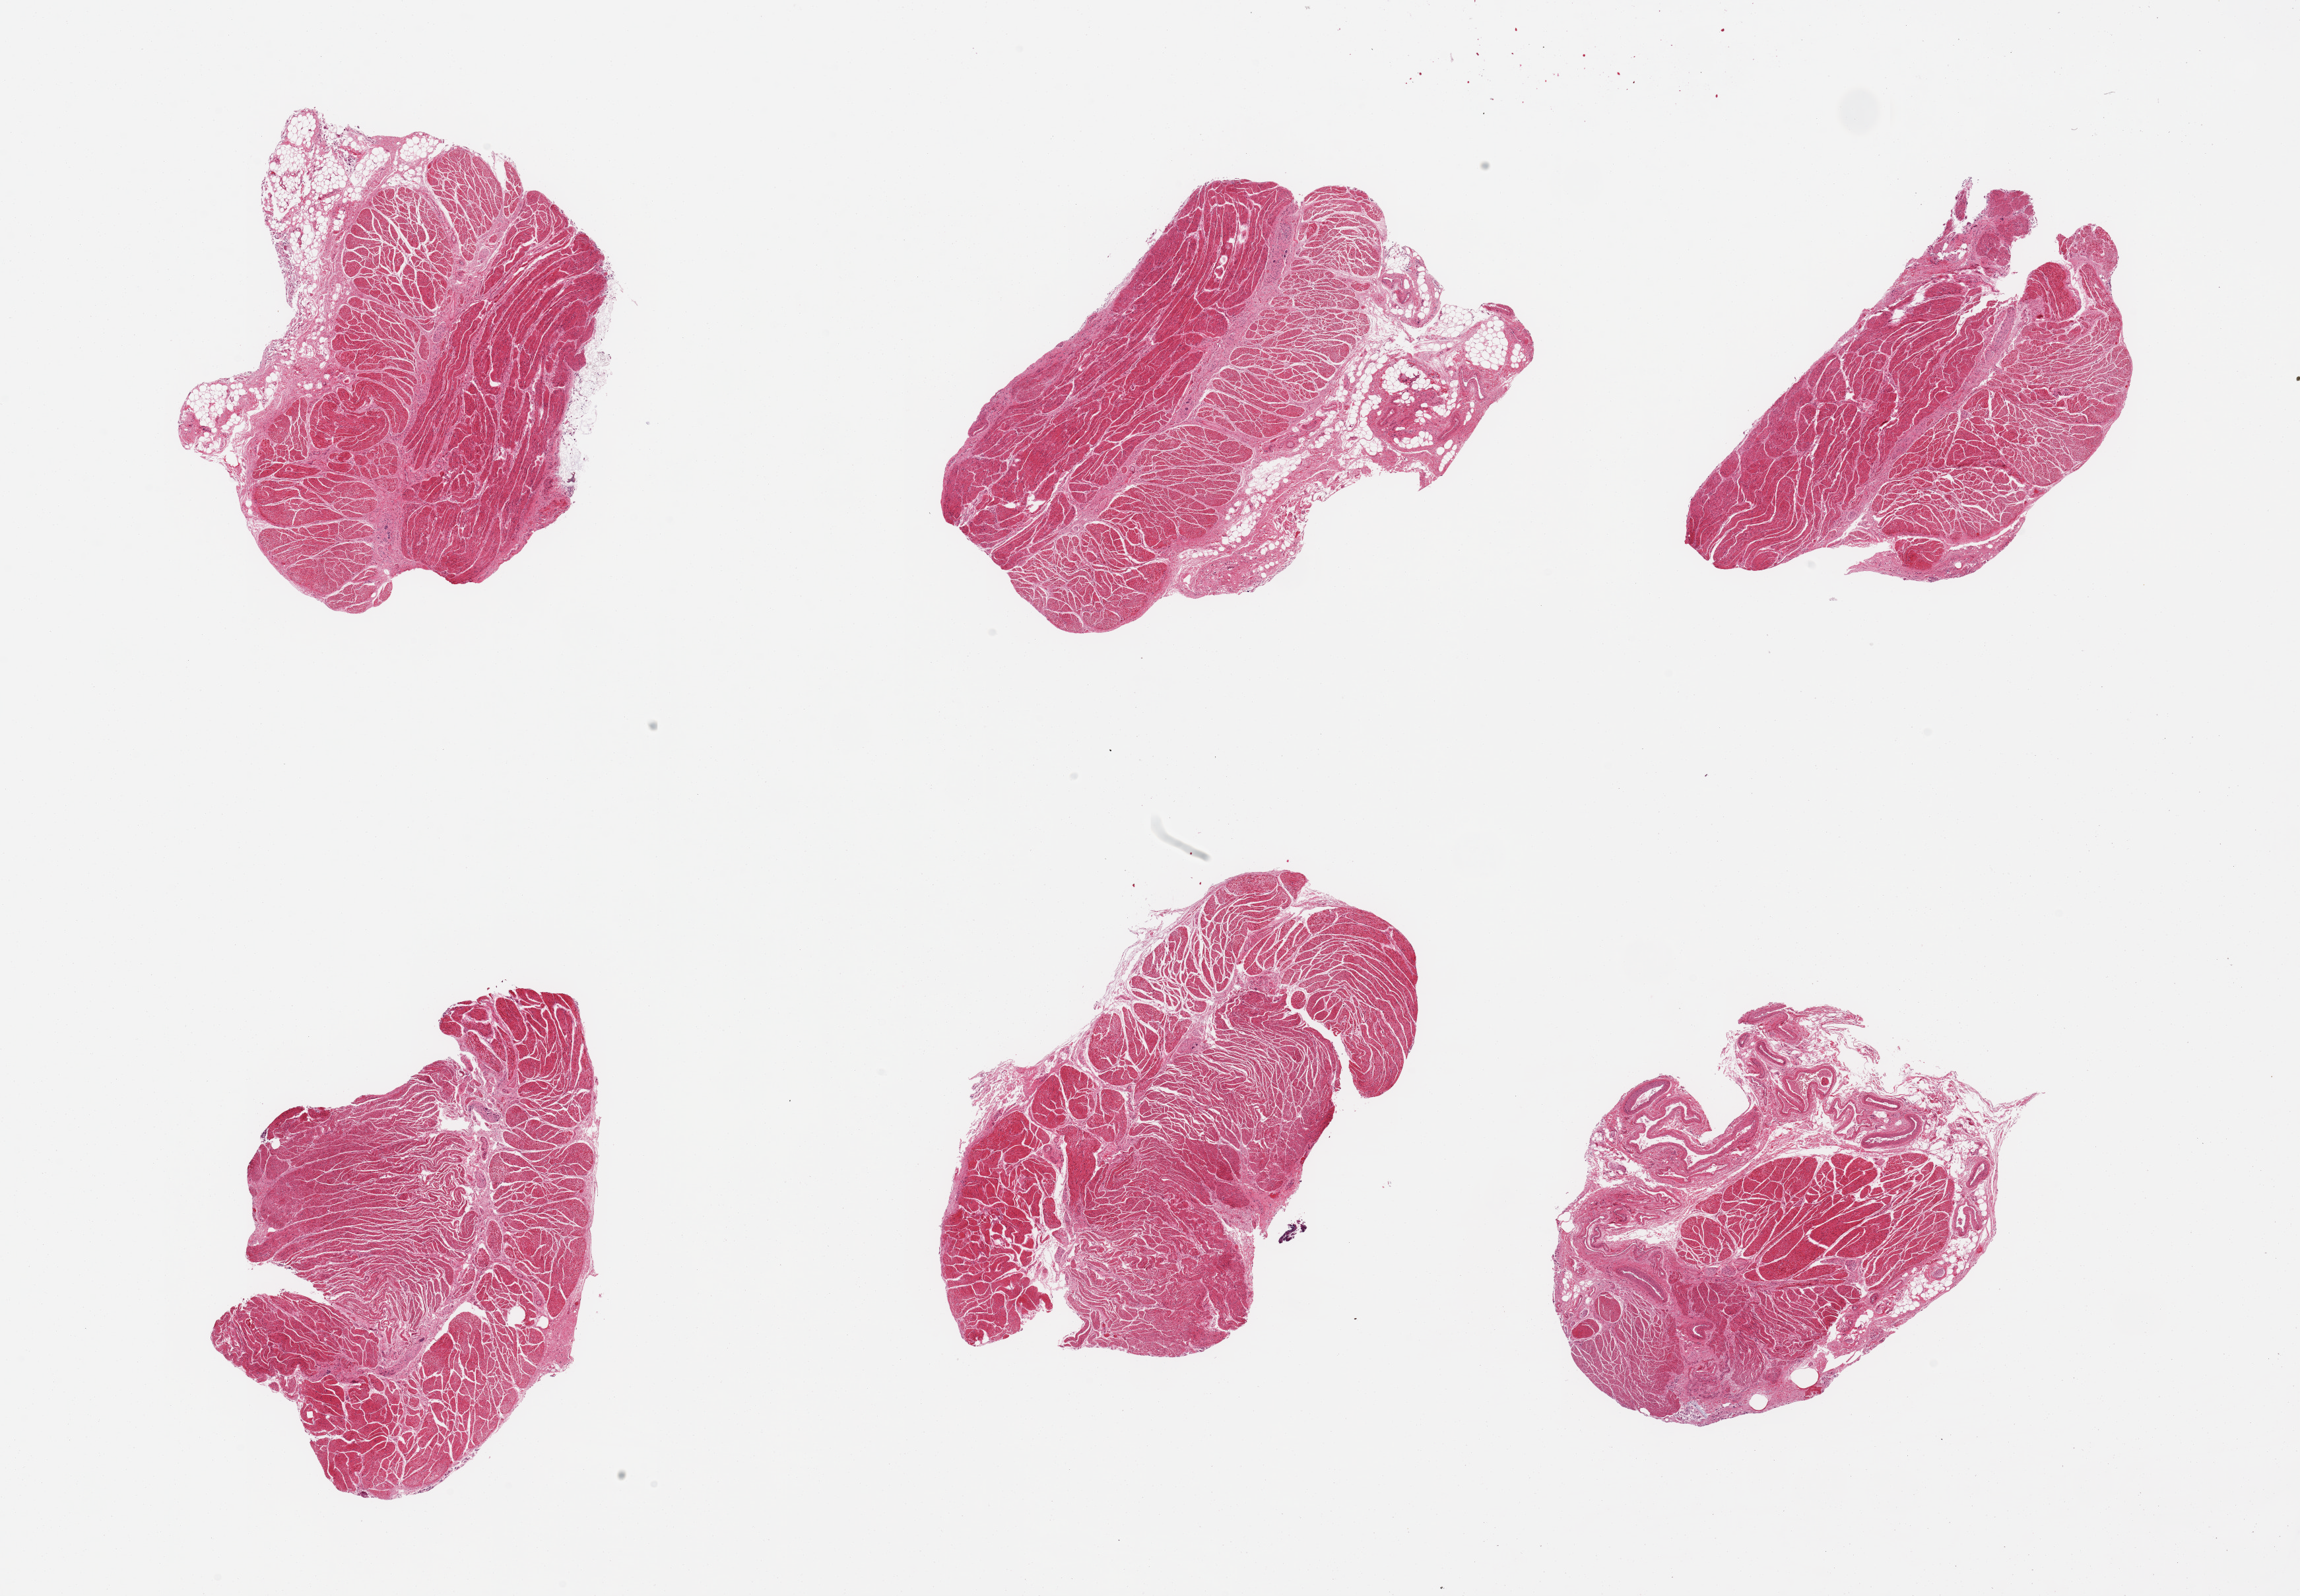
Digitized haematoxylin and eosin-stained section, whole scanned area (about 27.6 x 19.1 mm, slide scanned at 20x) shown as a low-resolution overview; PAXgene-fixed, paraffin-embedded tissue; section of gastroesophageal junction (target tissue); tissue donor sample. Male donor.
Pathologist's review note for this sample: 6 pieces, confirmed target muscularis; adherent fat up to ~1mm.